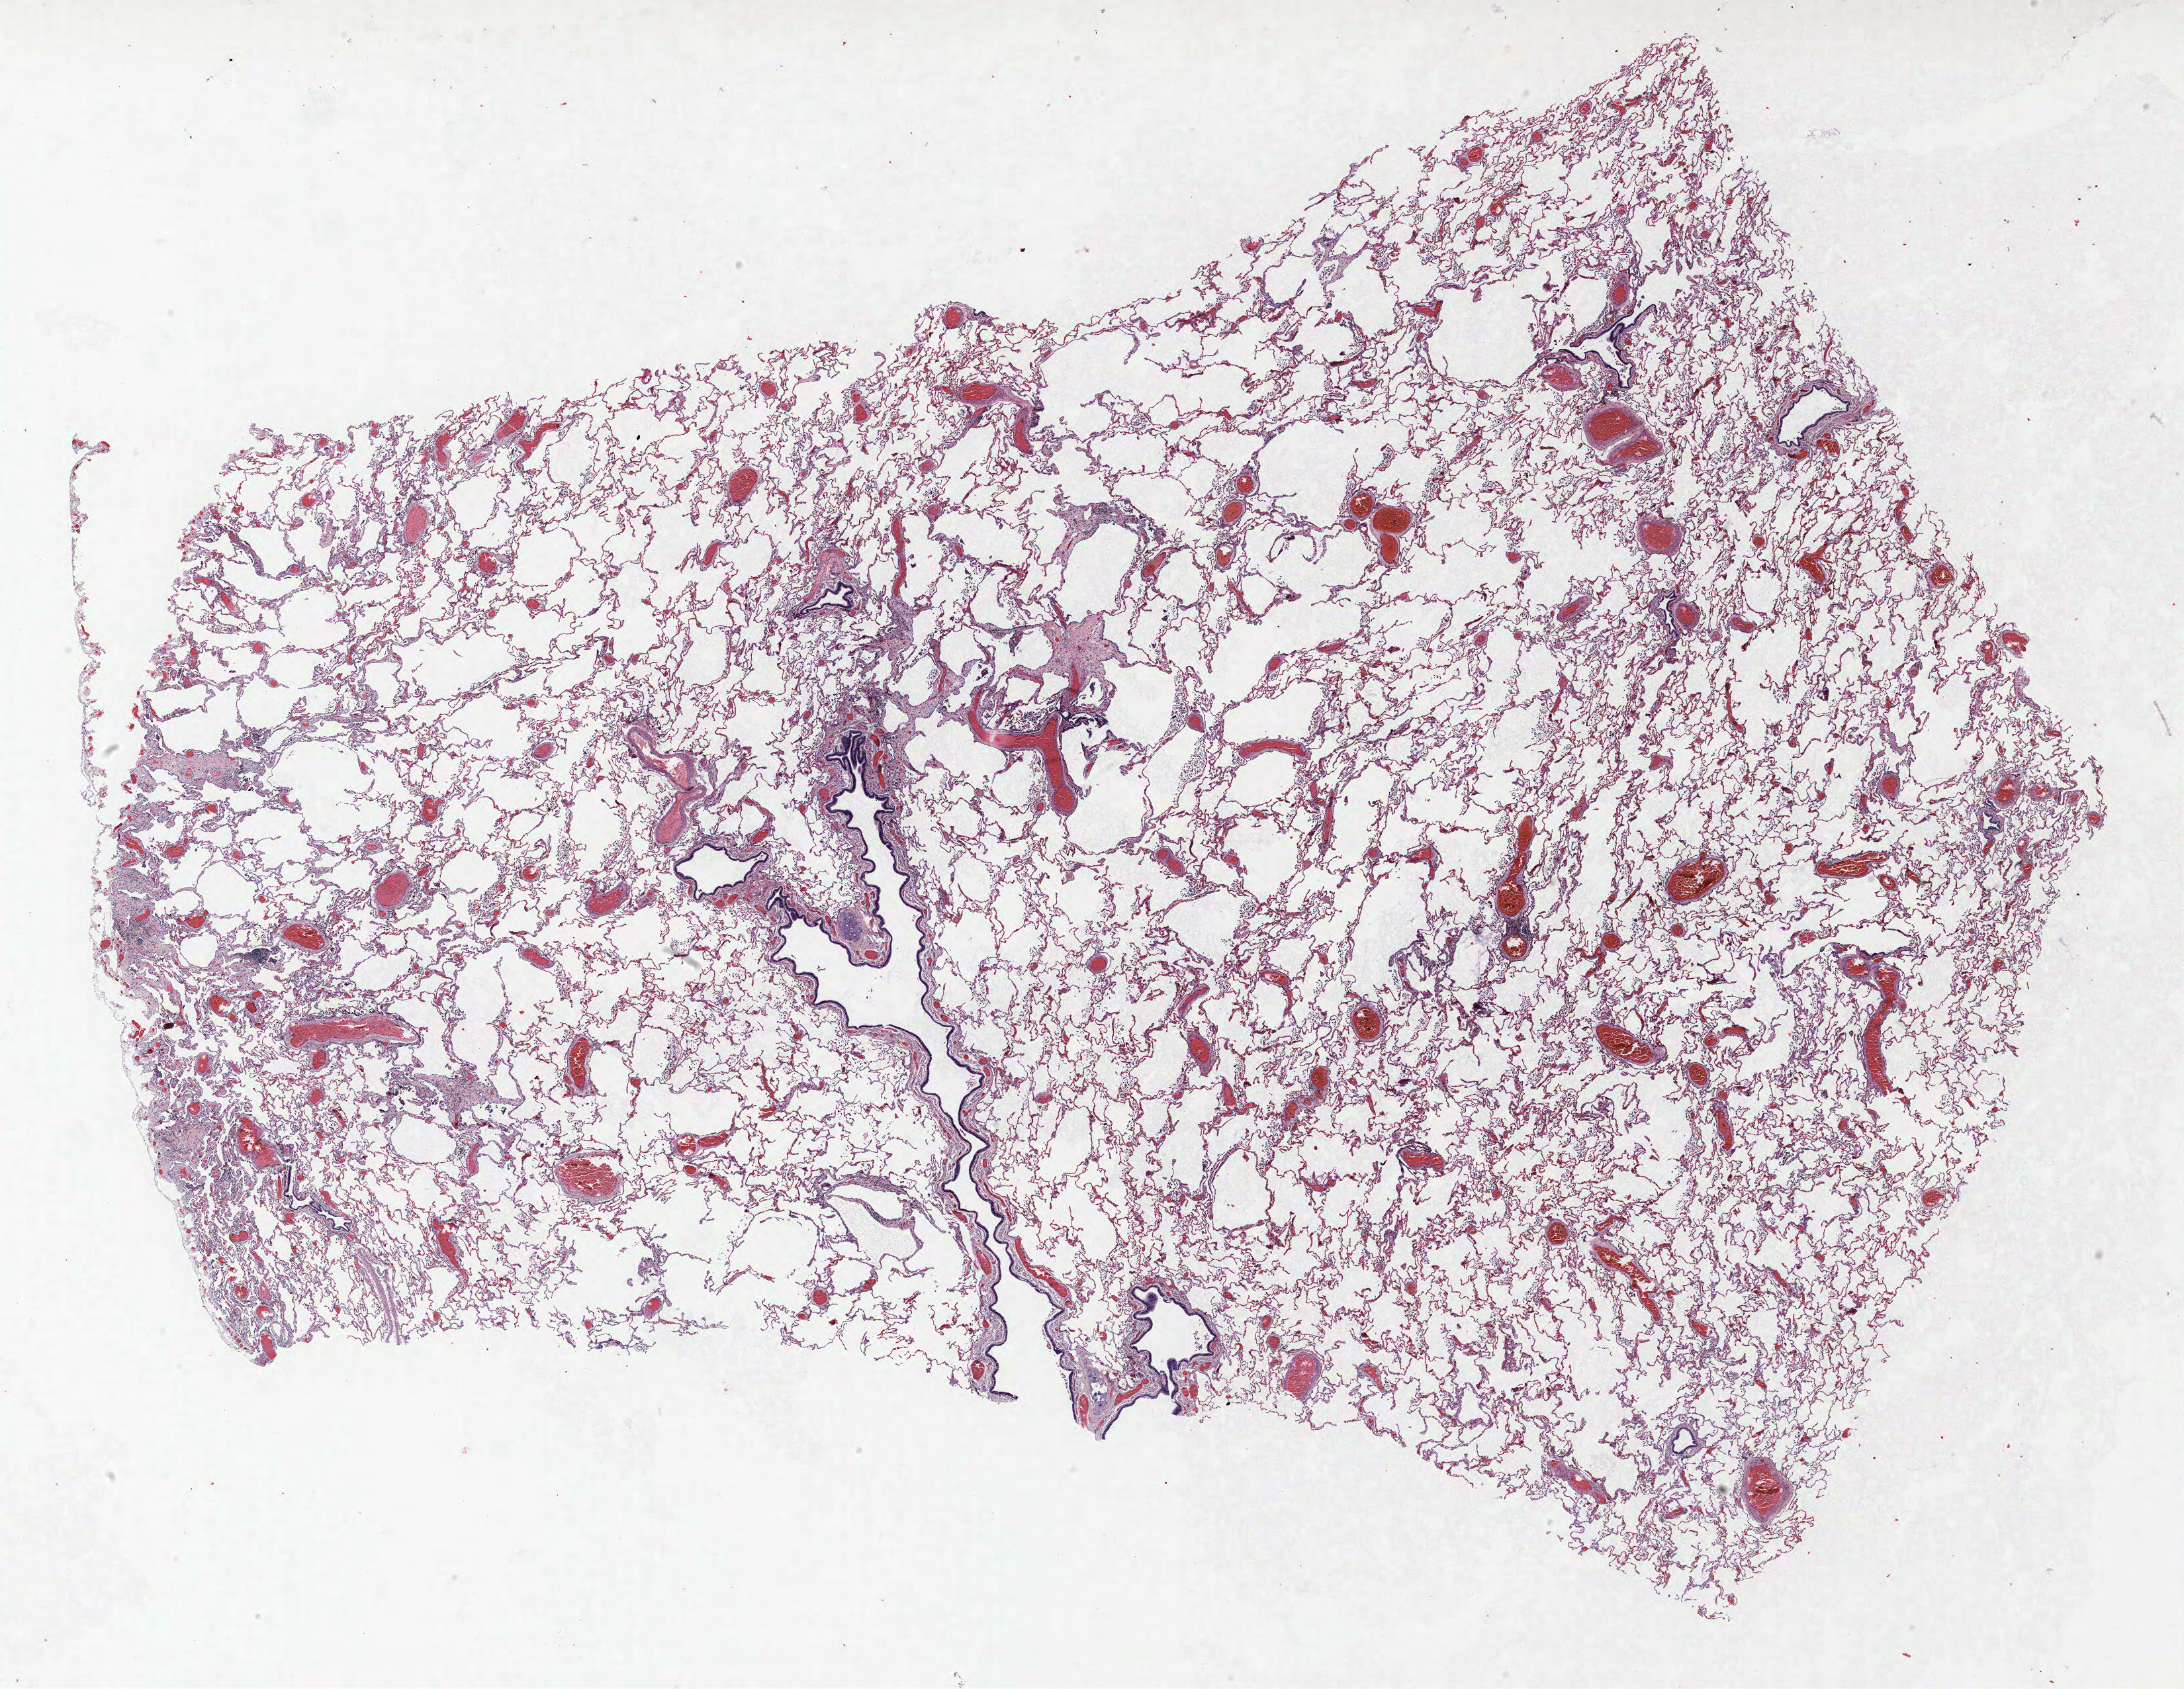
Whole-slide histology image, Hematoxylin and eosin (H&E) stained, a low-resolution overview of the entire scanned area, about 26.4 x 20.4 mm (from a 40x scan), formalin-fixed paraffin-embedded (FFPE) section, lung. Male, age 64 at enrolment. Grade: poorly differentiated (G3).
Tumour size (pathology): 20 mm. Primary tumour location (clinical record): right middle lobe. Stage (AJCC 6th edition): IIIA. Participant's lung-cancer diagnosis: Non-small cell carcinoma.